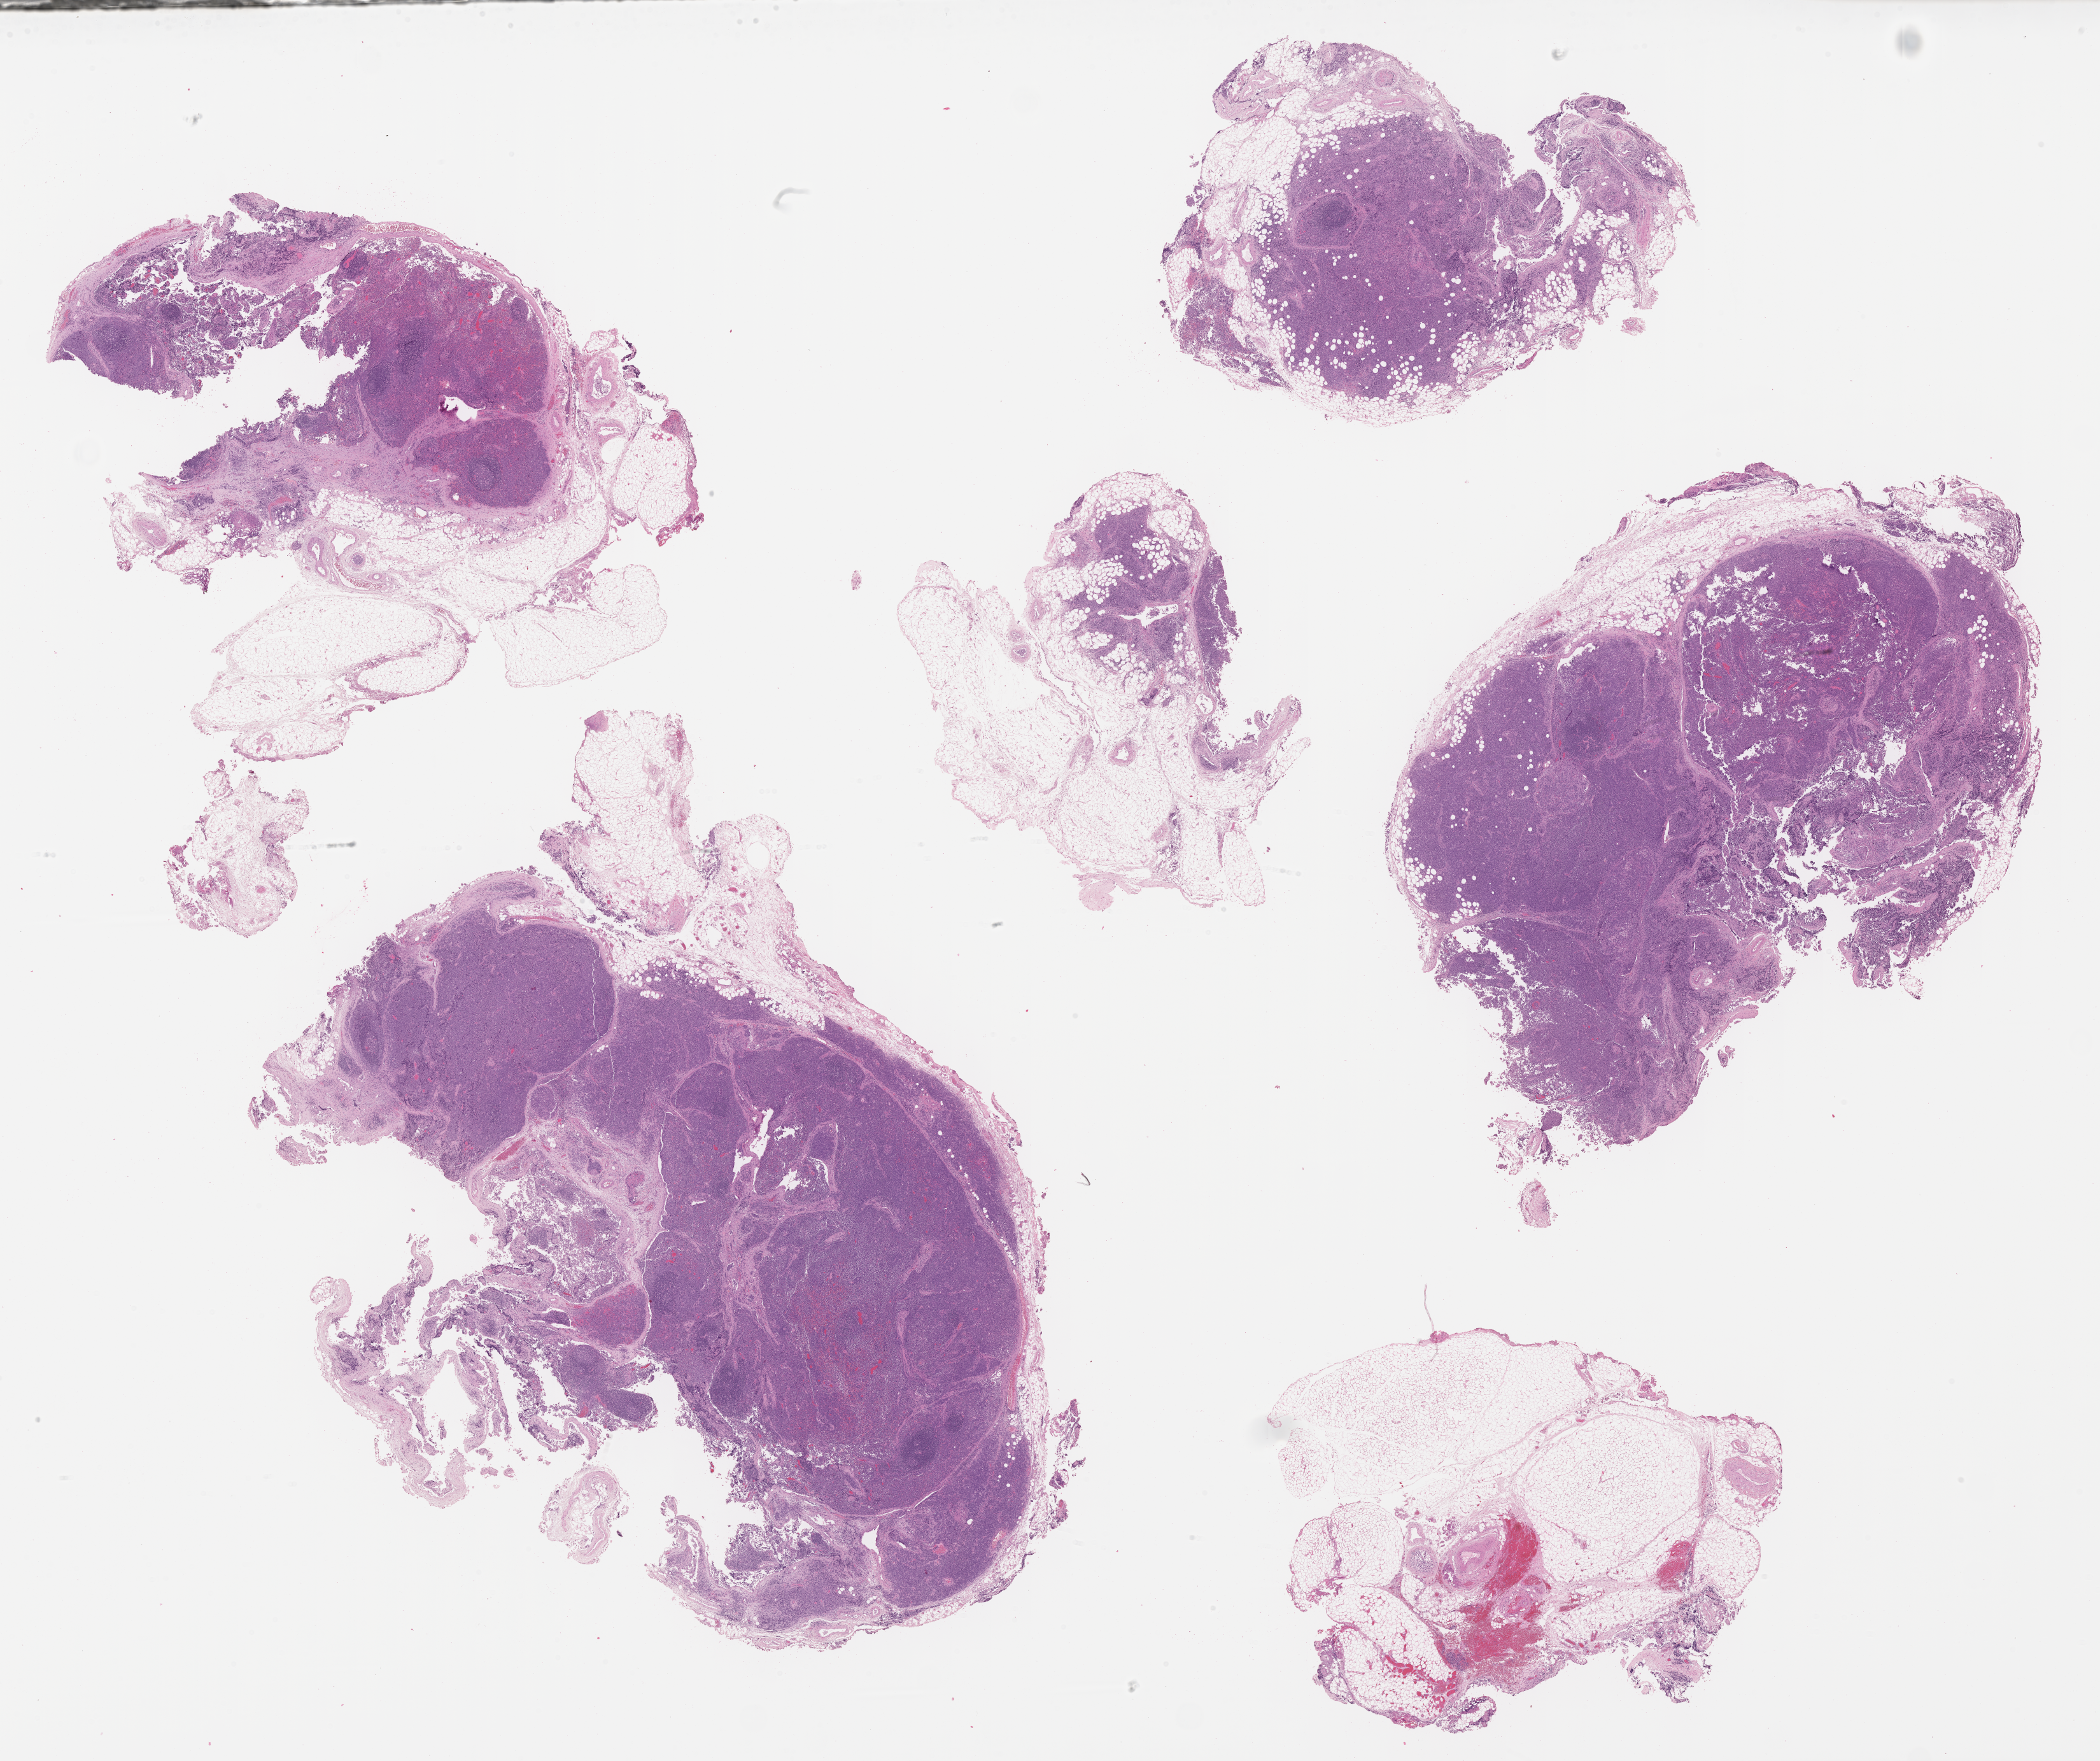
Digitized H&E-stained section of tumor tissue, low-resolution overview of the scanned area, about 26.7 x 22.4 mm, formalin-fixed paraffin-embedded section, sample anatomic site: lymph node (metastatic site). Patient: male, age 17.9 years at diagnosis.
Diagnosis: rhabdomyosarcoma; histological classification: embryonal rhabdomyosarcoma.